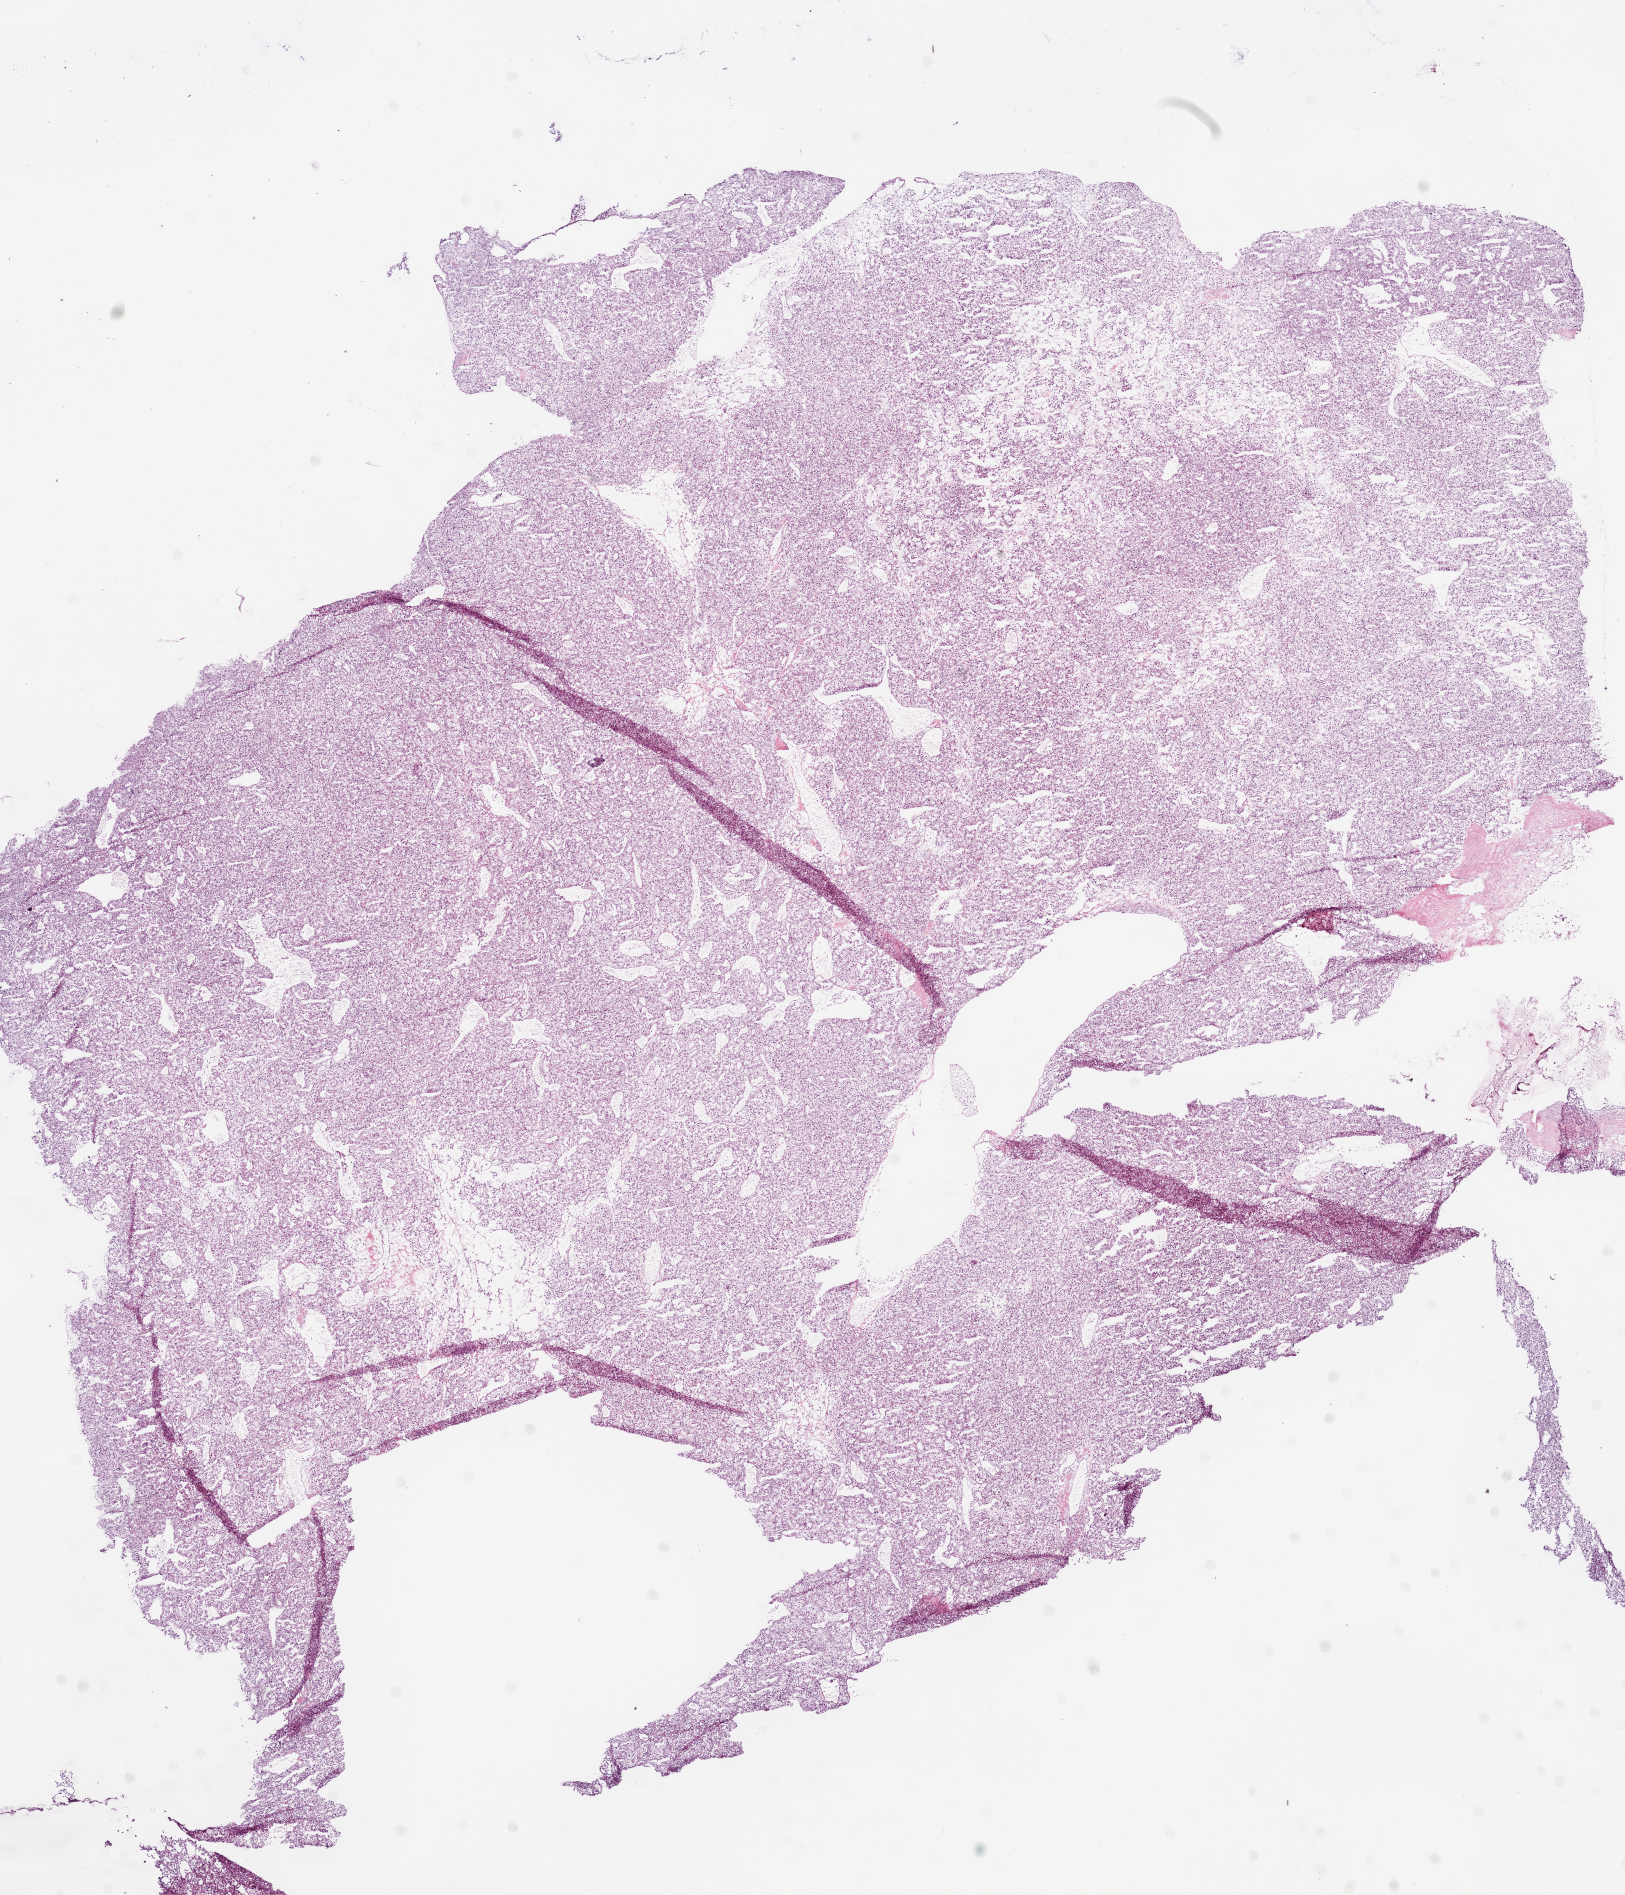
H&E whole-slide image — a low-resolution overview of the entire scanned area, about 13.0 x 15.2 mm. Frozen section from the bottom of the tissue portion. Kidney, primary tumour sample. Patient: male, age at initial diagnosis 47 years. Histologic grade: G3 (poorly differentiated). Composition of this section per pathologist review: tumour cells 90%, tumour nuclei 85%, normal cells 0%, stromal cells 10%, necrosis 0%.
• laterality: right
• AJCC pathologic stage: III
• pathologic diagnosis: Clear cell adenocarcinoma, NOS